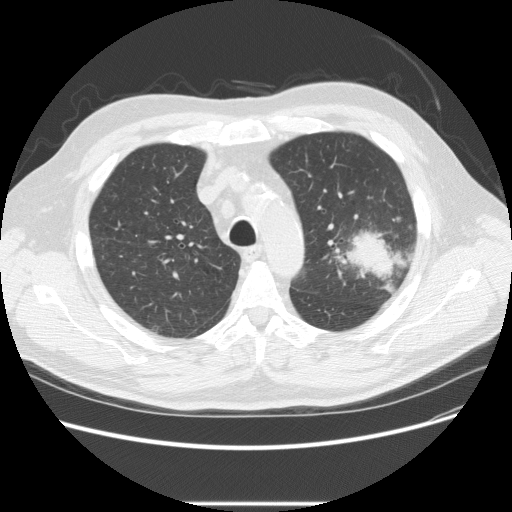
Axial slice from a low-dose chest CT screening exam, first (baseline) screen, lung window (W 1500 / L -600 HU). Male participant, aged 73 years at enrolment. Former smoker at enrolment.
Expert reader's lesion annotation, bounding box [x1, y1, x2, y2] px = [332, 215, 417, 286]. The screening reader recorded 2 non-calcified nodules or masses ≥4 mm on this exam; which of them this box marks is not recorded. Official screen result: positive, change unspecified: nodule(s) >= 4 mm or enlarging nodule(s), mass(es), or other non-specific abnormalities suspicious for lung cancer. Lung cancer was diagnosed 11 days after this screen: bronchiolo-alveolar adenocarcinoma, NOS, other location, well differentiated (G1), stage IV (AJCC 6th edition).